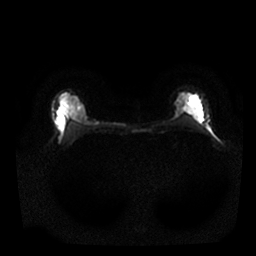
Breast MRI, one axial slice; slice 16 of 25 in the series (ordered by position); diffusion-weighted series; image 2 of 4 stored at this slice position (different b-values; order by instance number); 1.5 T; 4 mm slice thickness; 256 × 256 image matrix. Female patient.
Outlined on this slice (expert manual segmentation):
- tumour on diffusion-weighted imaging: bounding box (x1, y1, x2, y2) in pixels: (175, 108, 180, 116)